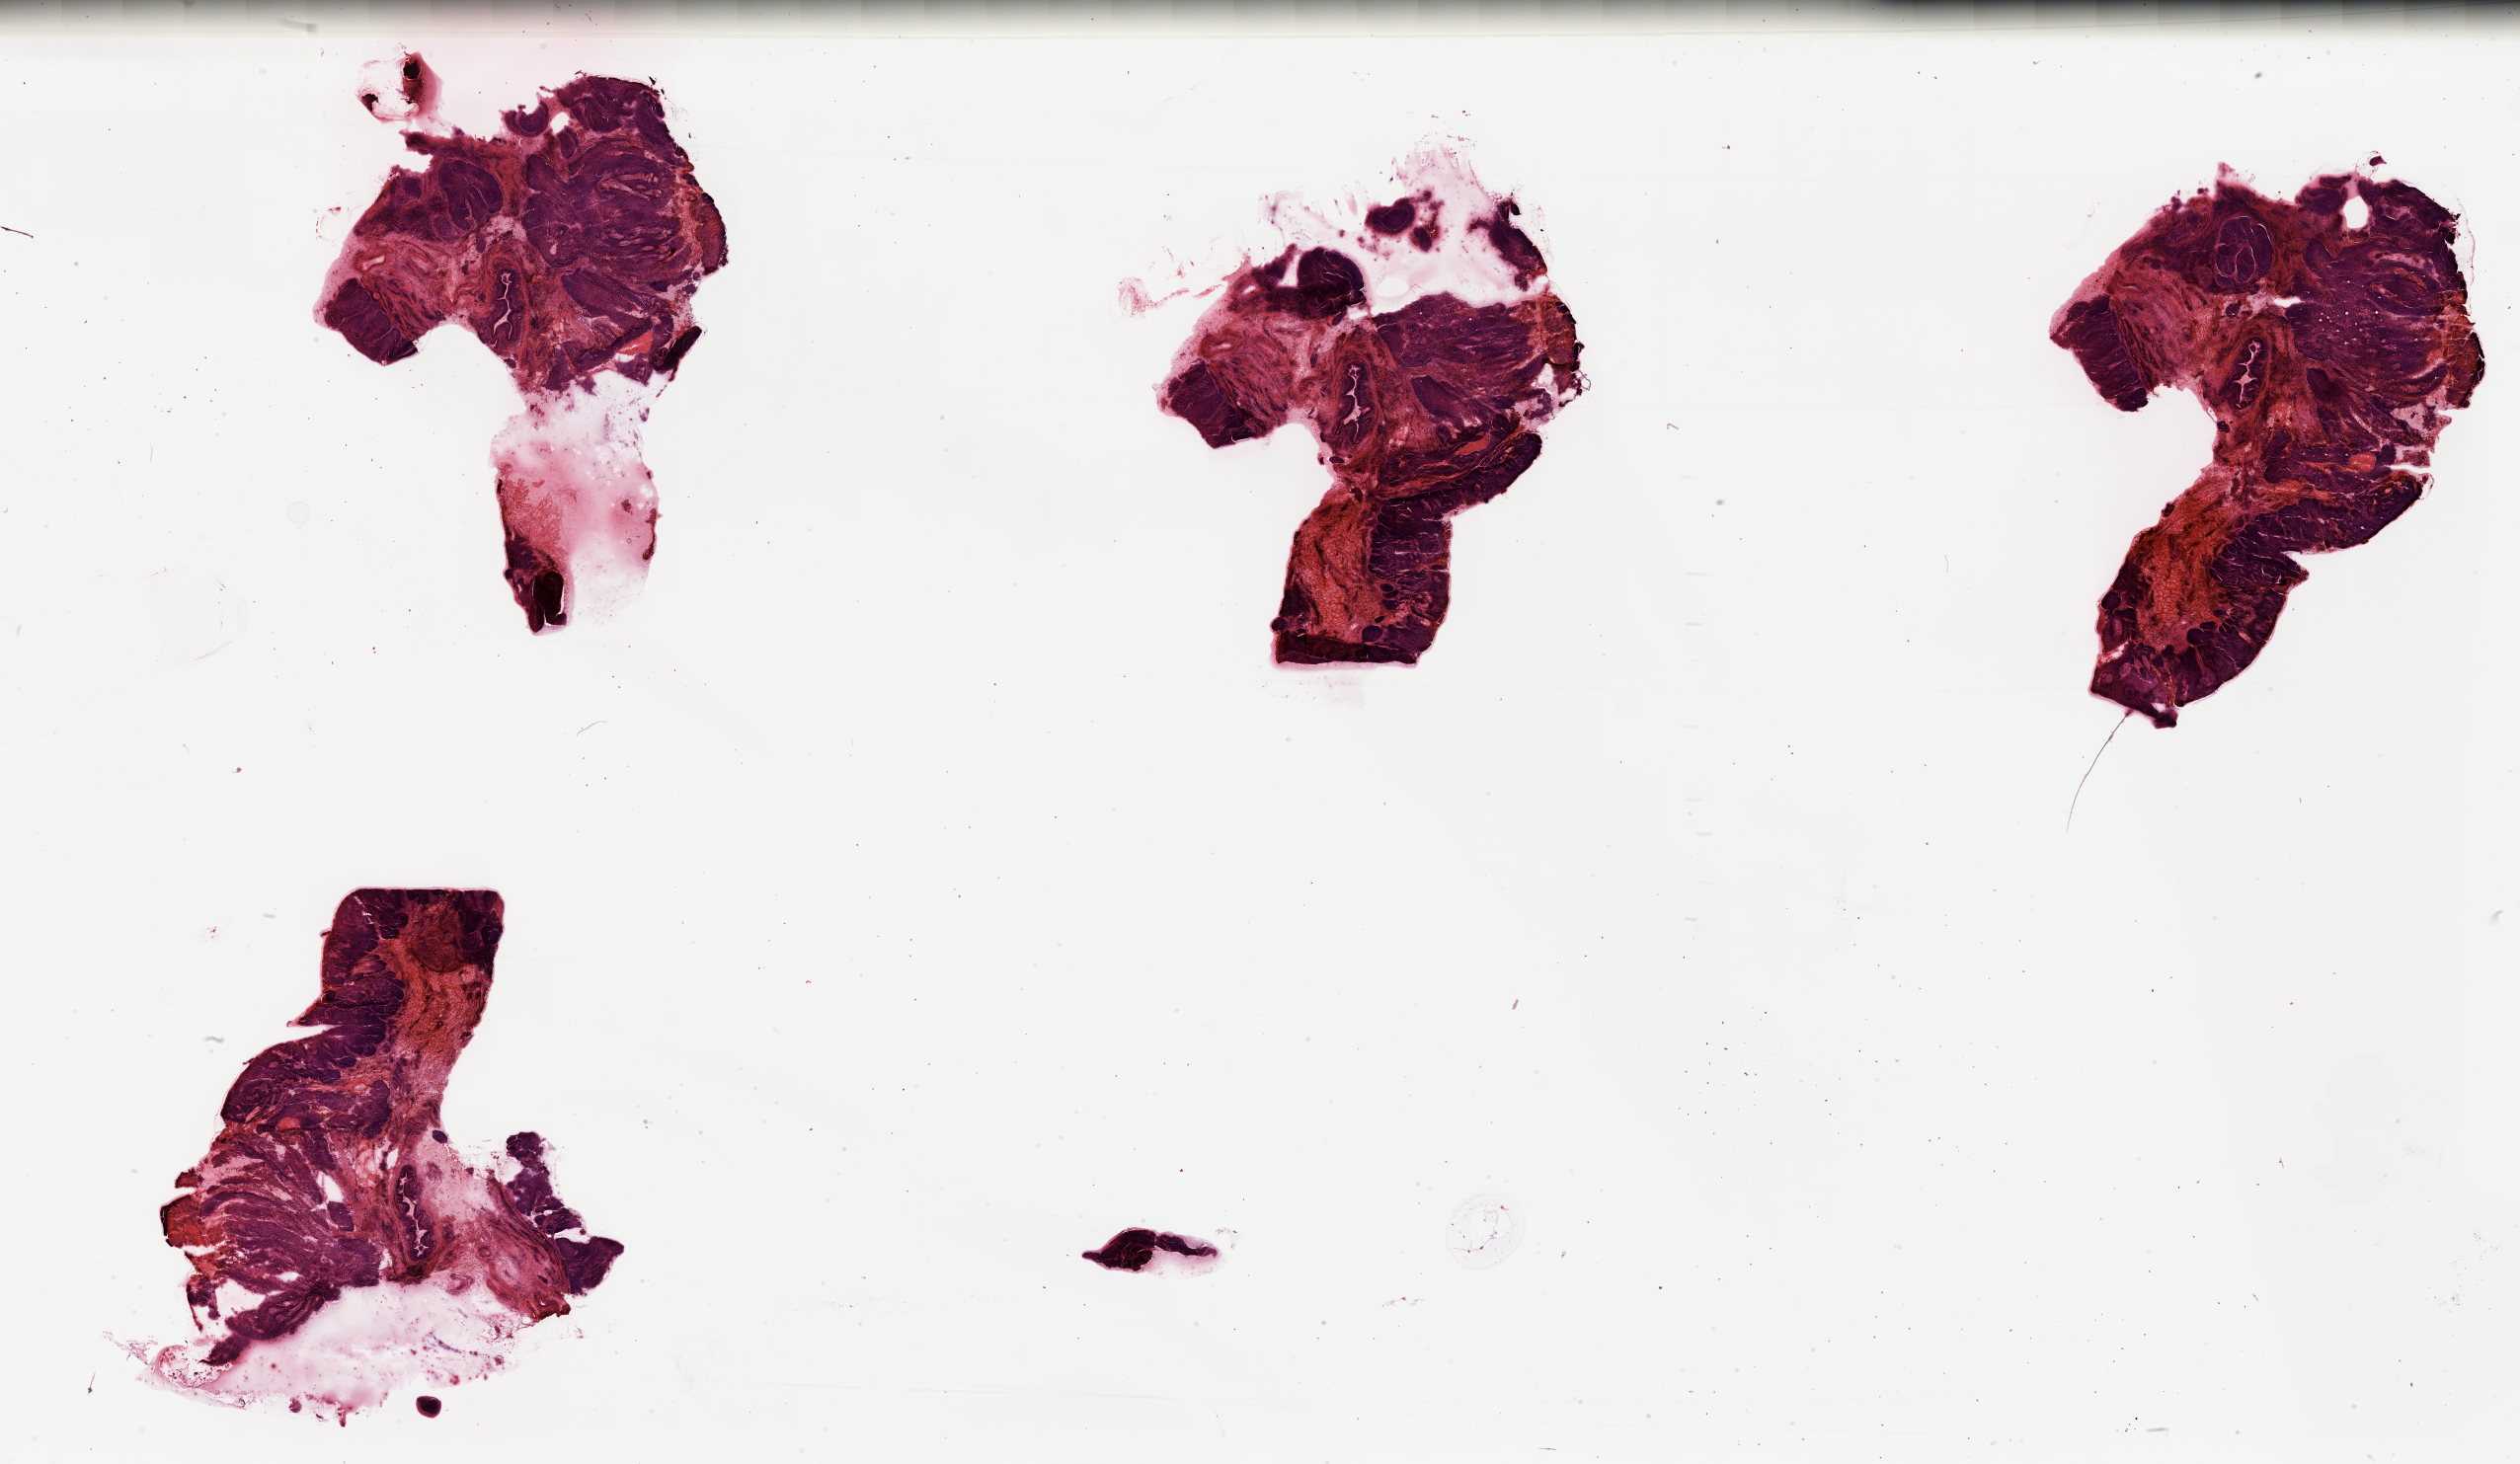
Whole-slide histology image, H&E, shown as a low-resolution overview of the whole scanned area (about 40.4 x 23.5 mm). Tumour tissue sample, sampled site: oral cavity. 63-year-old male patient. Histologic grade: G2 (moderately differentiated). Composition of this section per pathologist review: tumour nuclei 80%, necrosis 10%.
* AJCC pathologic stage: III
* diagnosis: Squamous cell carcinoma, NOS (overlapping lesion of lip, oral cavity and pharynx)
* primary tumour site (as recorded): oral cavity